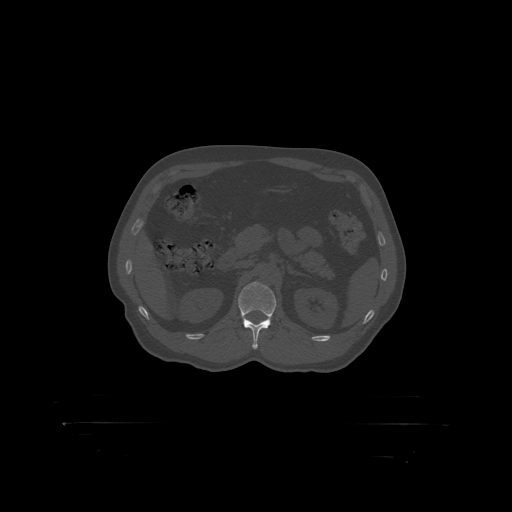
CT including the spine, one axial slice. Slice 323 of 399 in the series (ordered by position). Reconstruction kernel STANDARD. 120 kVp. Bone window (W 1800 / L 400 HU). 1.25 mm slice thickness. 512 × 512 image matrix, field of view 650 × 650 mm. Male patient, age 46 years. Case-level facts recorded for this patient, not image findings: primary cancer: skin.
Outlined on this slice (semi-automatic segmentation, software-assisted and operator-edited):
- L1 vertebra: box from (x=238, y=282) to (x=277, y=317) px